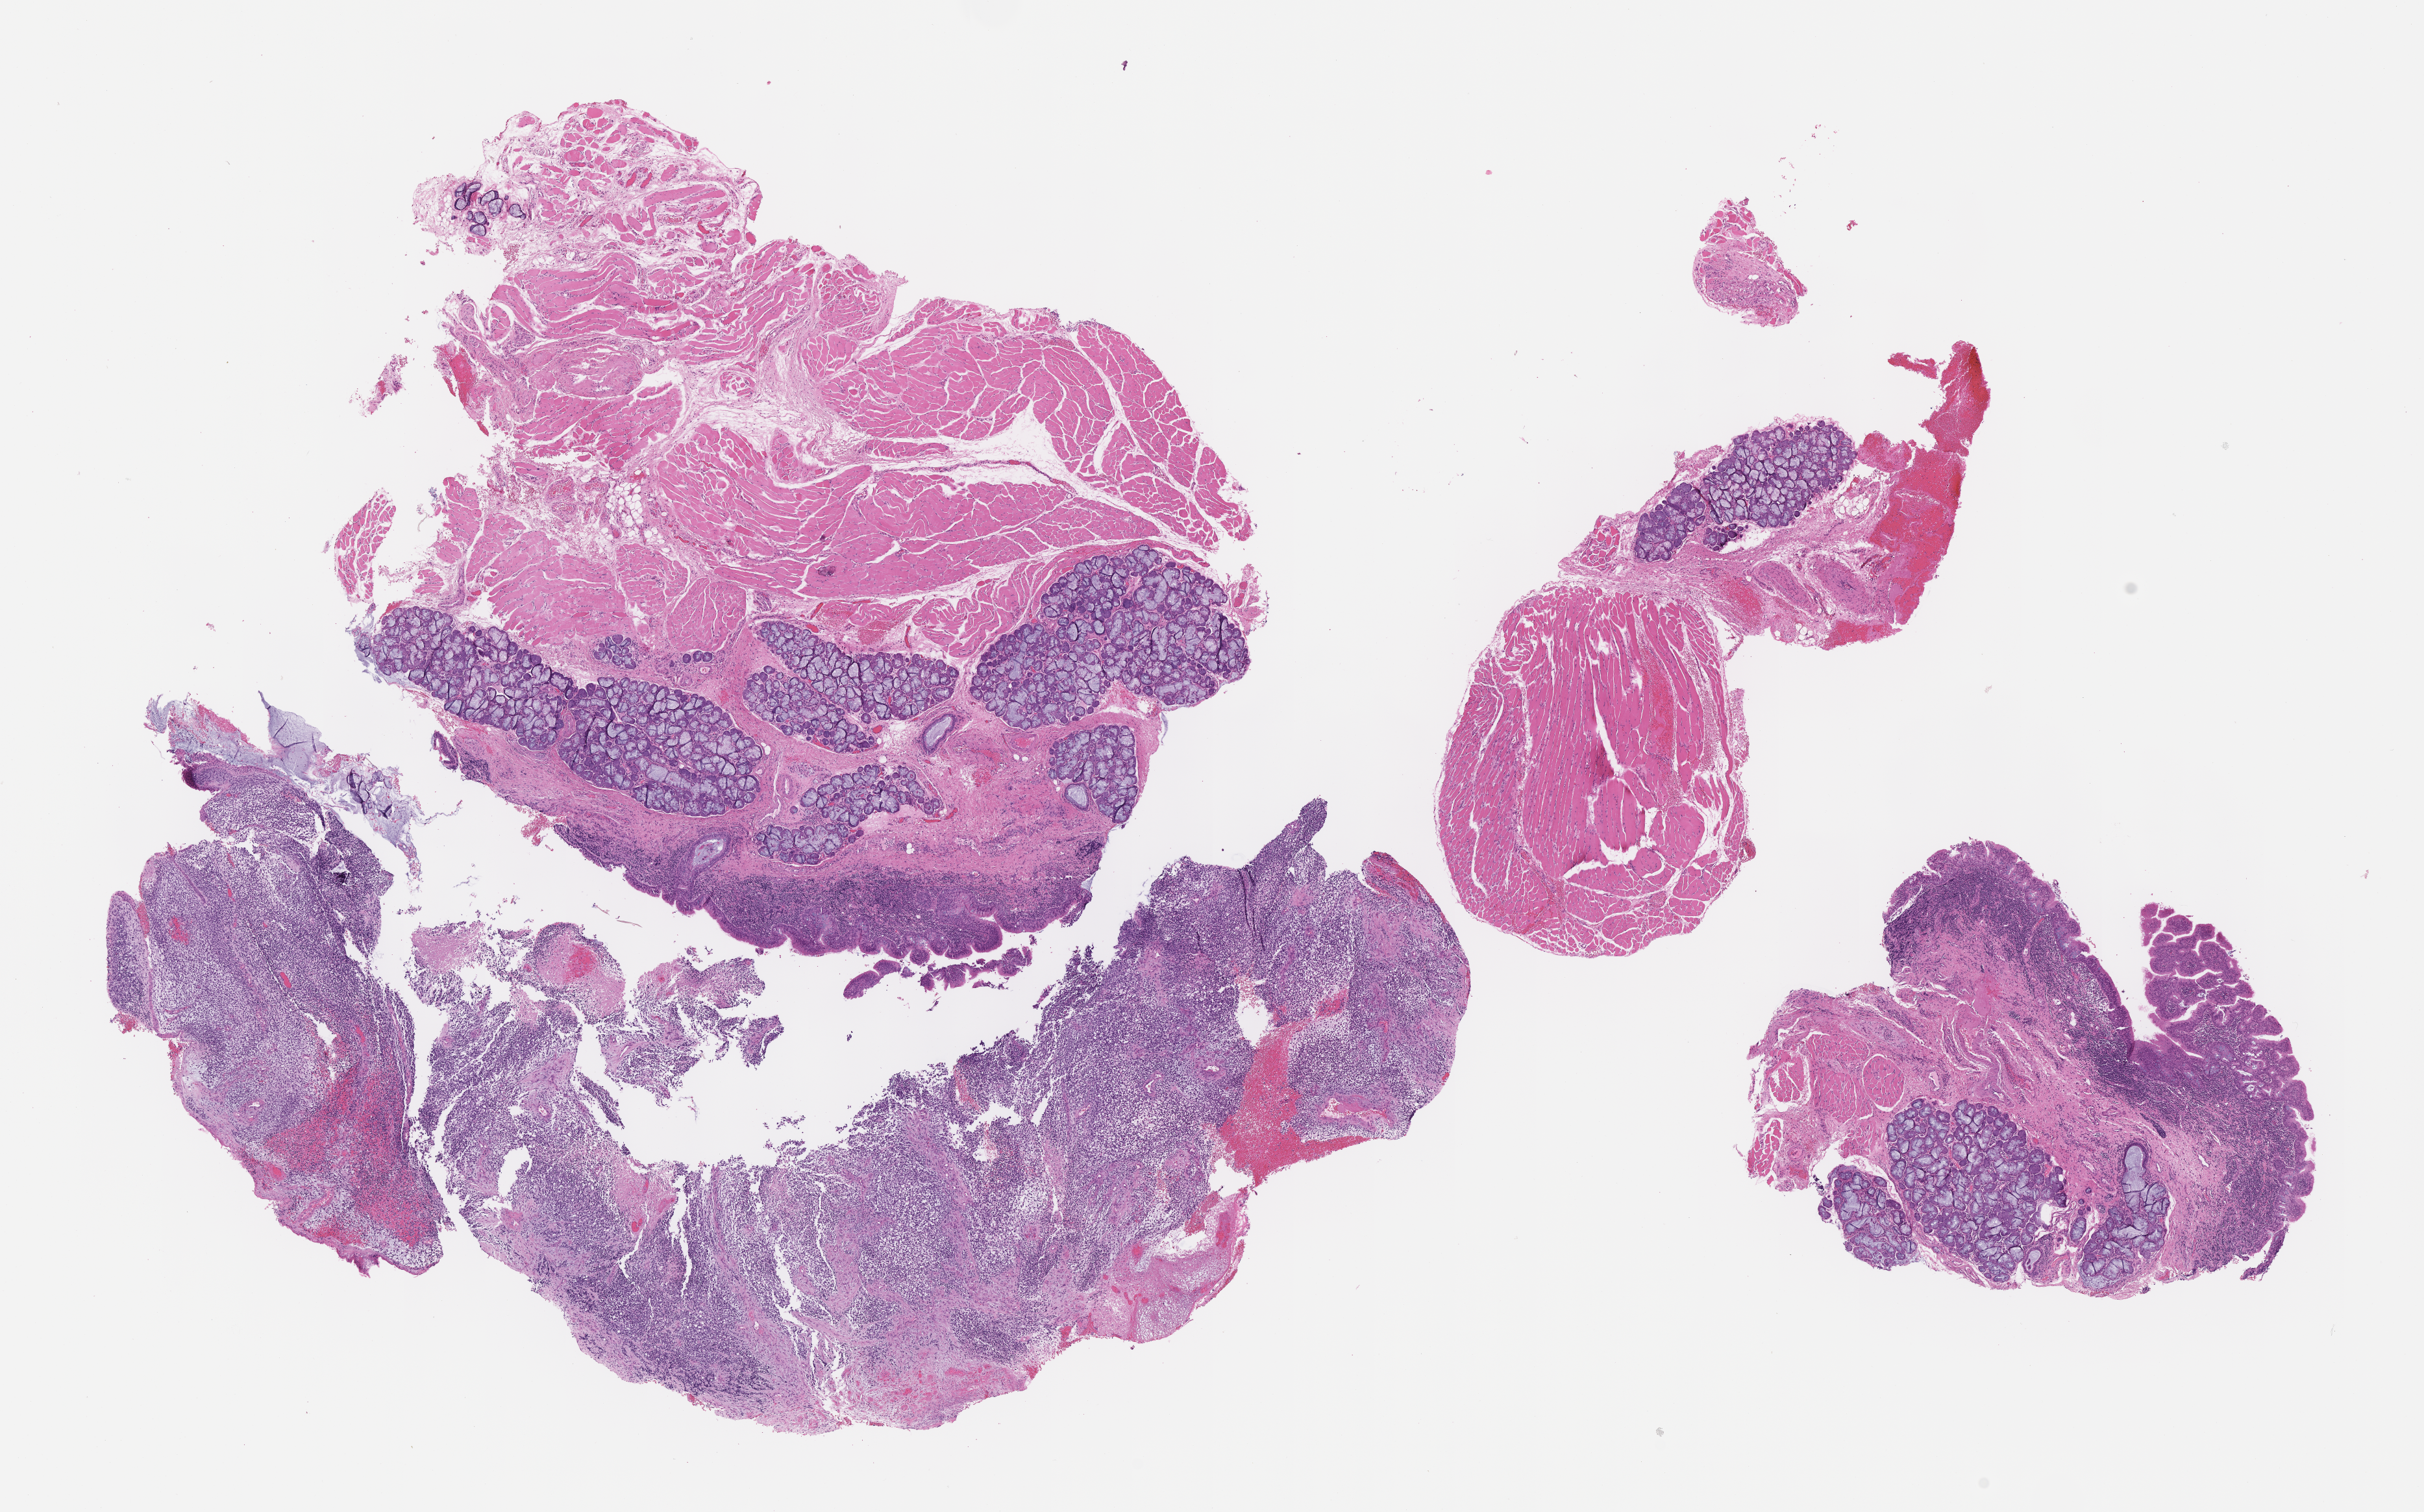
Digitized hematoxylin and eosin (H&E)-stained section of tumor tissue, a low-resolution overview of the entire scanned area, about 15.1 x 9.4 mm. Formalin-fixed, paraffin-embedded (FFPE) tissue. Site: oropharynx. Patient: male, age 12.2 years at diagnosis.
Stage (as recorded): 3. Diagnosis: rhabdomyosarcoma; histological classification: embryonal rhabdomyosarcoma.